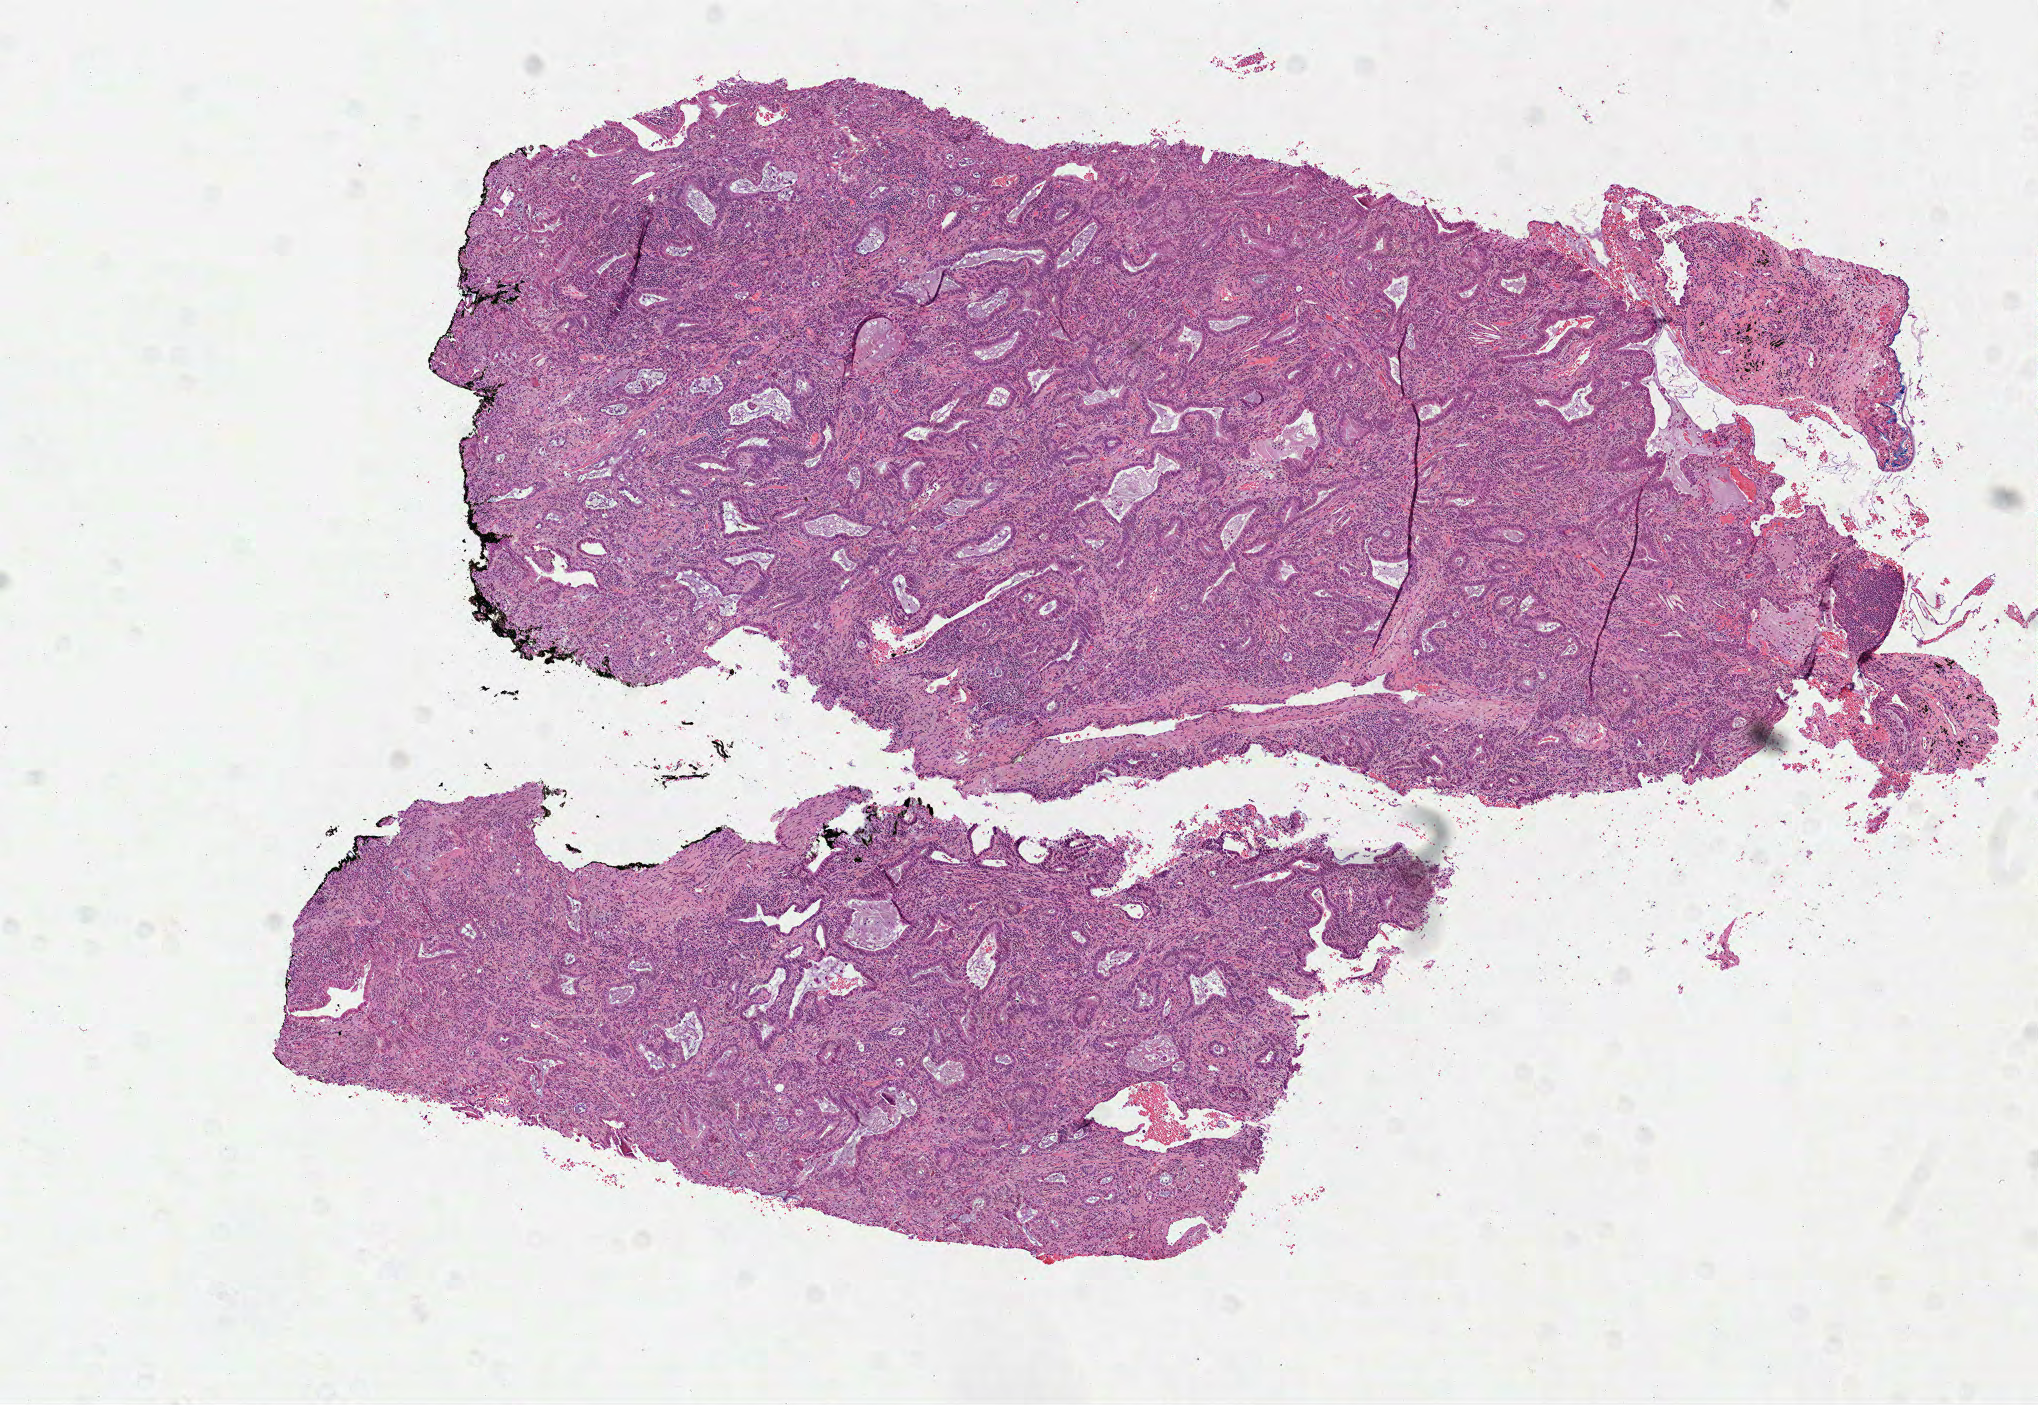
Digitized H&E-stained tissue section (whole slide) — whole scanned area (about 8.2 x 5.7 mm, slide scanned at 40x) shown as a low-resolution overview, formalin-fixed paraffin-embedded (FFPE) diagnostic section, lung, primary tumour sample. Male, age 75 years at initial diagnosis.
• AJCC pathologic stage: IIB (7th edition)
• laterality: right
• pathologic diagnosis: Adenocarcinoma, NOS (upper lobe, lung)